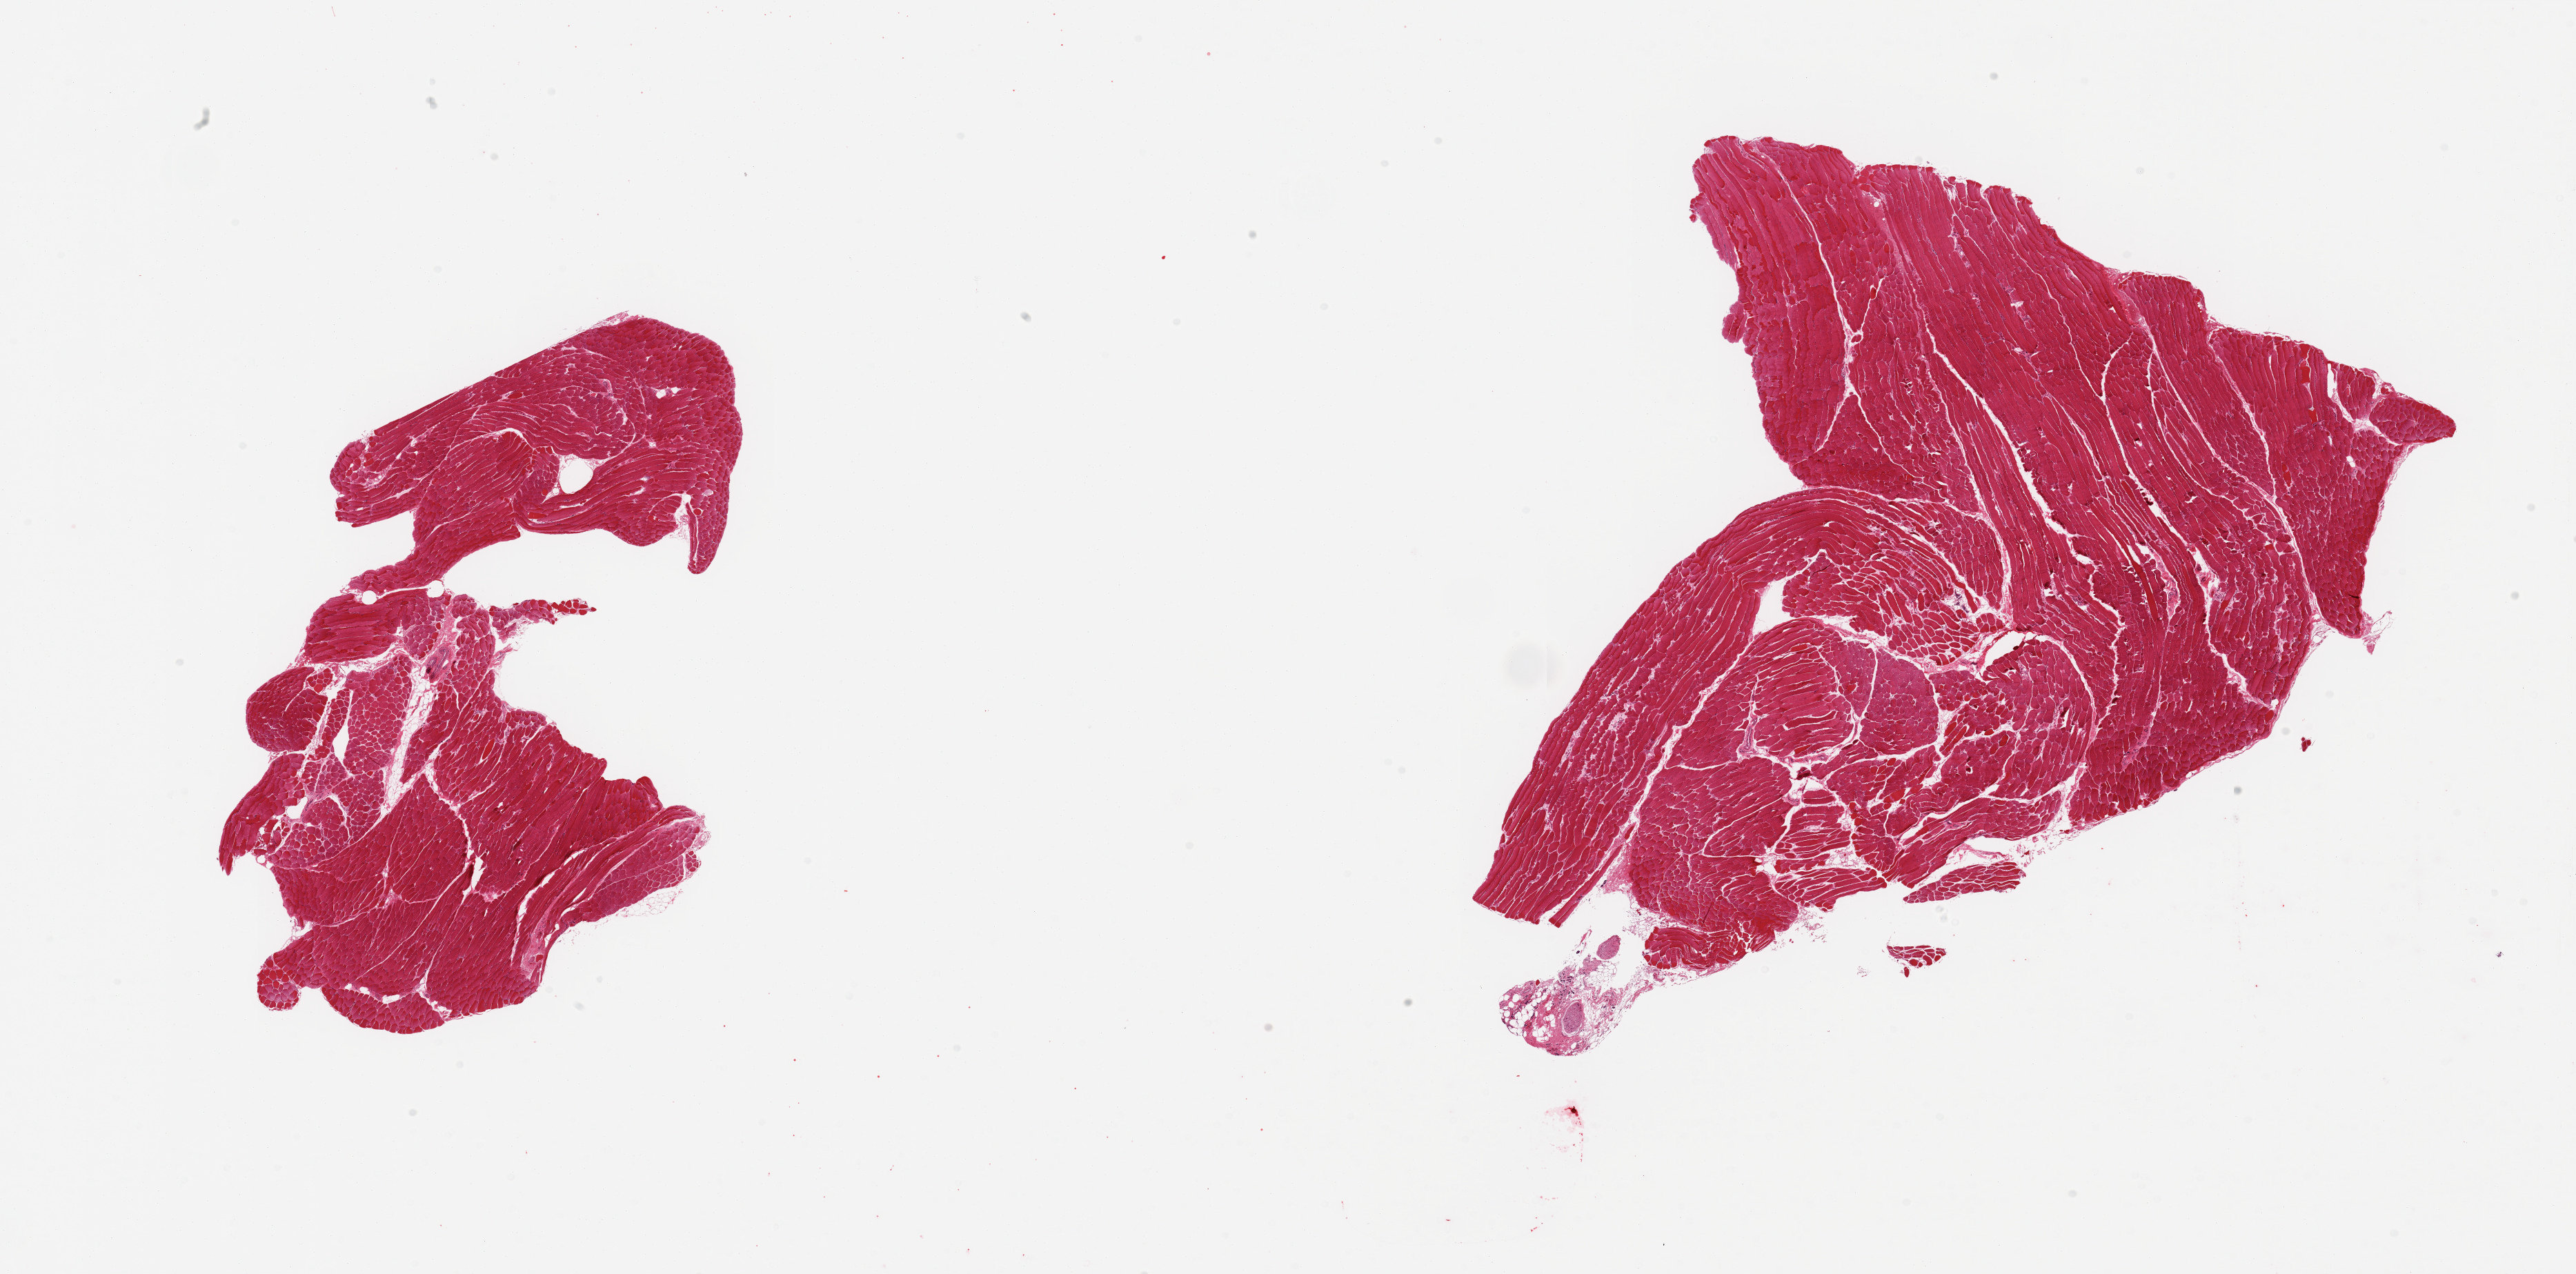
Hematoxylin and eosin (H&E) whole-slide image, a low-resolution overview of the entire scanned area, about 29.5 x 14.6 mm (from a 20x scan), PAXgene-fixed paraffin-embedded (PFPE) section, sampled site (target tissue): skeletal muscle, donor tissue sample. Donor: male.
Pathologist's review note for this sample: 2 pieces, focal peripheral nerve.